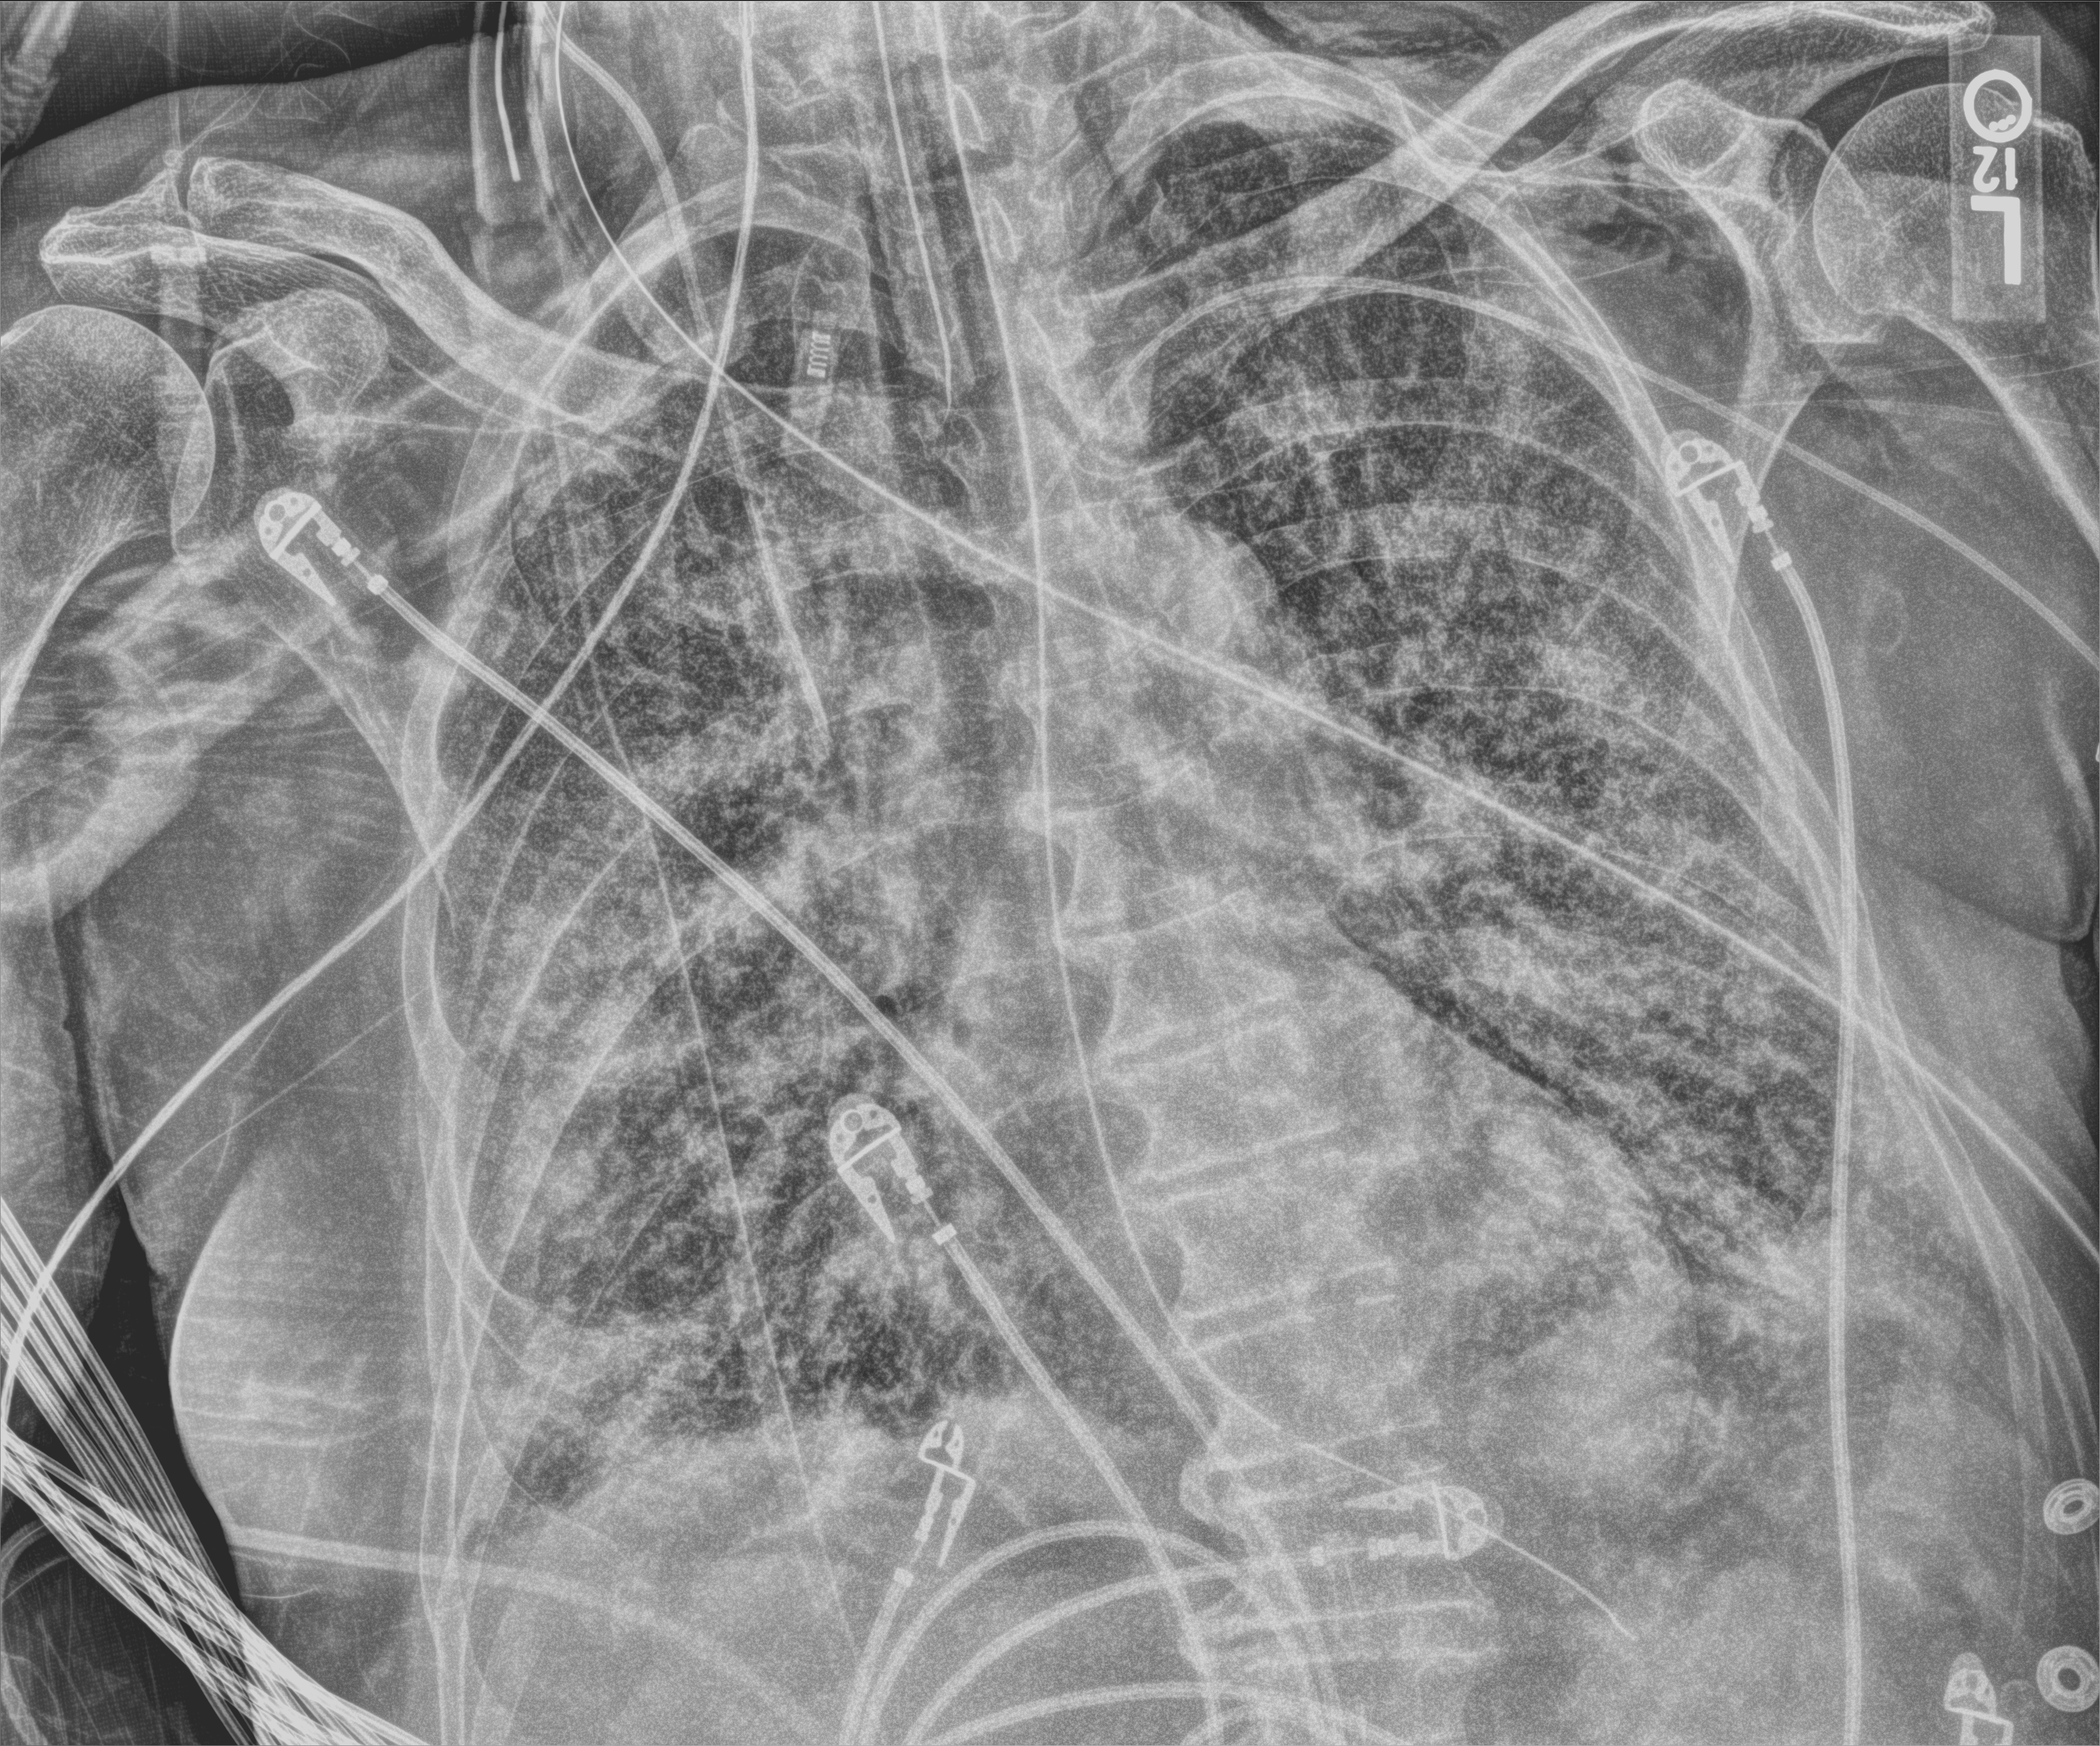
Bedside chest radiograph (computed radiography), anteroposterior (AP) projection. Male patient hospitalised with COVID-19, age 75–90 years.
Hospital-stay facts (about this admission, not read from this image; timing relative to this image not recorded):
- mechanically ventilated during this hospital stay: yes
- length of hospital stay: 47 days